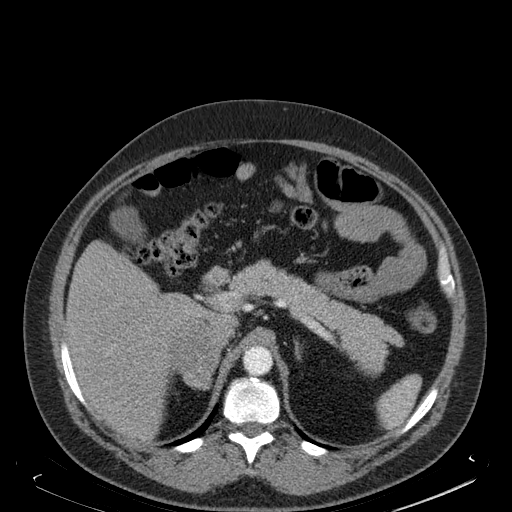
Contrast-enhanced abdominal CT, one axial slice. Position 120 of 181 along the scan axis. Soft-tissue window (W 400 / L 40 HU). 512 × 512 image matrix, field of view 405 × 405 mm. Male patient. Case-level facts recorded for this patient, not image findings: diagnosis: adrenocortical carcinoma; tumour side: right adrenal; tumour size at pathology: 7.5 cm; Ki-67 index: 25 %; stage (as recorded): 4.
Structures marked on this image (semi-automatic segmentation, software-assisted and operator-edited):
- mass: box from (x=169, y=319) to (x=219, y=387) px